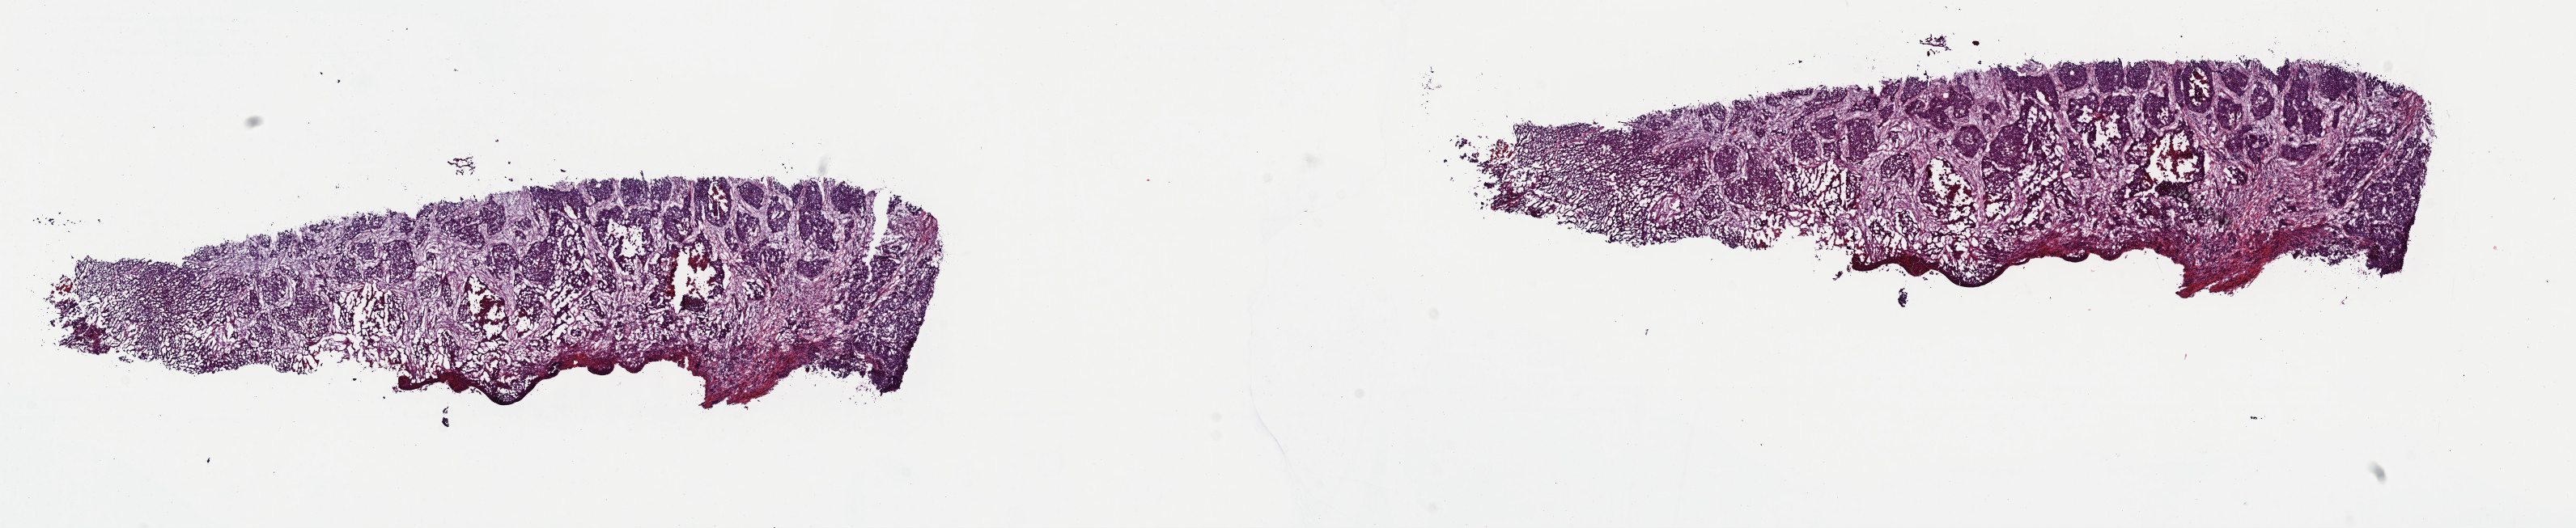
Hematoxylin and eosin (H&E) stained whole-slide image, low-resolution overview of the scanned area, about 25.1 x 5.2 mm (slide scanned at 40x), frozen section, primary tumour sample from the lung. Patient: male, age at initial diagnosis 48 years. Slide review estimates, as recorded: tumour cells 90%, tumour nuclei 75%, normal cells 0%, stromal cells 0%, necrosis 10%. Inflammatory infiltration, as recorded: lymphocyte infiltration 0%, monocyte infiltration 0%, neutrophil infiltration 0%.
Pathologic diagnosis: Adenocarcinoma, NOS. AJCC pathologic stage: IIA.